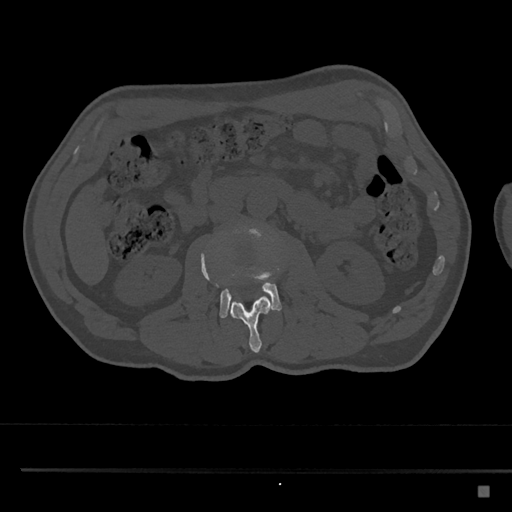
CT including the spine, one axial slice. Slice 732 of 797 in the series (ordered by position). Reconstruction kernel Br40s/3. Bone window (W 1800 / L 400 HU). 0.5 mm slice thickness. 512 × 512 image matrix, field of view 391 × 391 mm. Patient: male, 59 years. From the clinical record (not read from this slice): primary cancer: prostate.
Structures marked on this image (semi-automatic segmentation, software-assisted and operator-edited):
- L2 vertebra: bounding box [x1, y1, x2, y2] px = [201, 253, 272, 353]
- L3 vertebra: [201, 220, 282, 319]